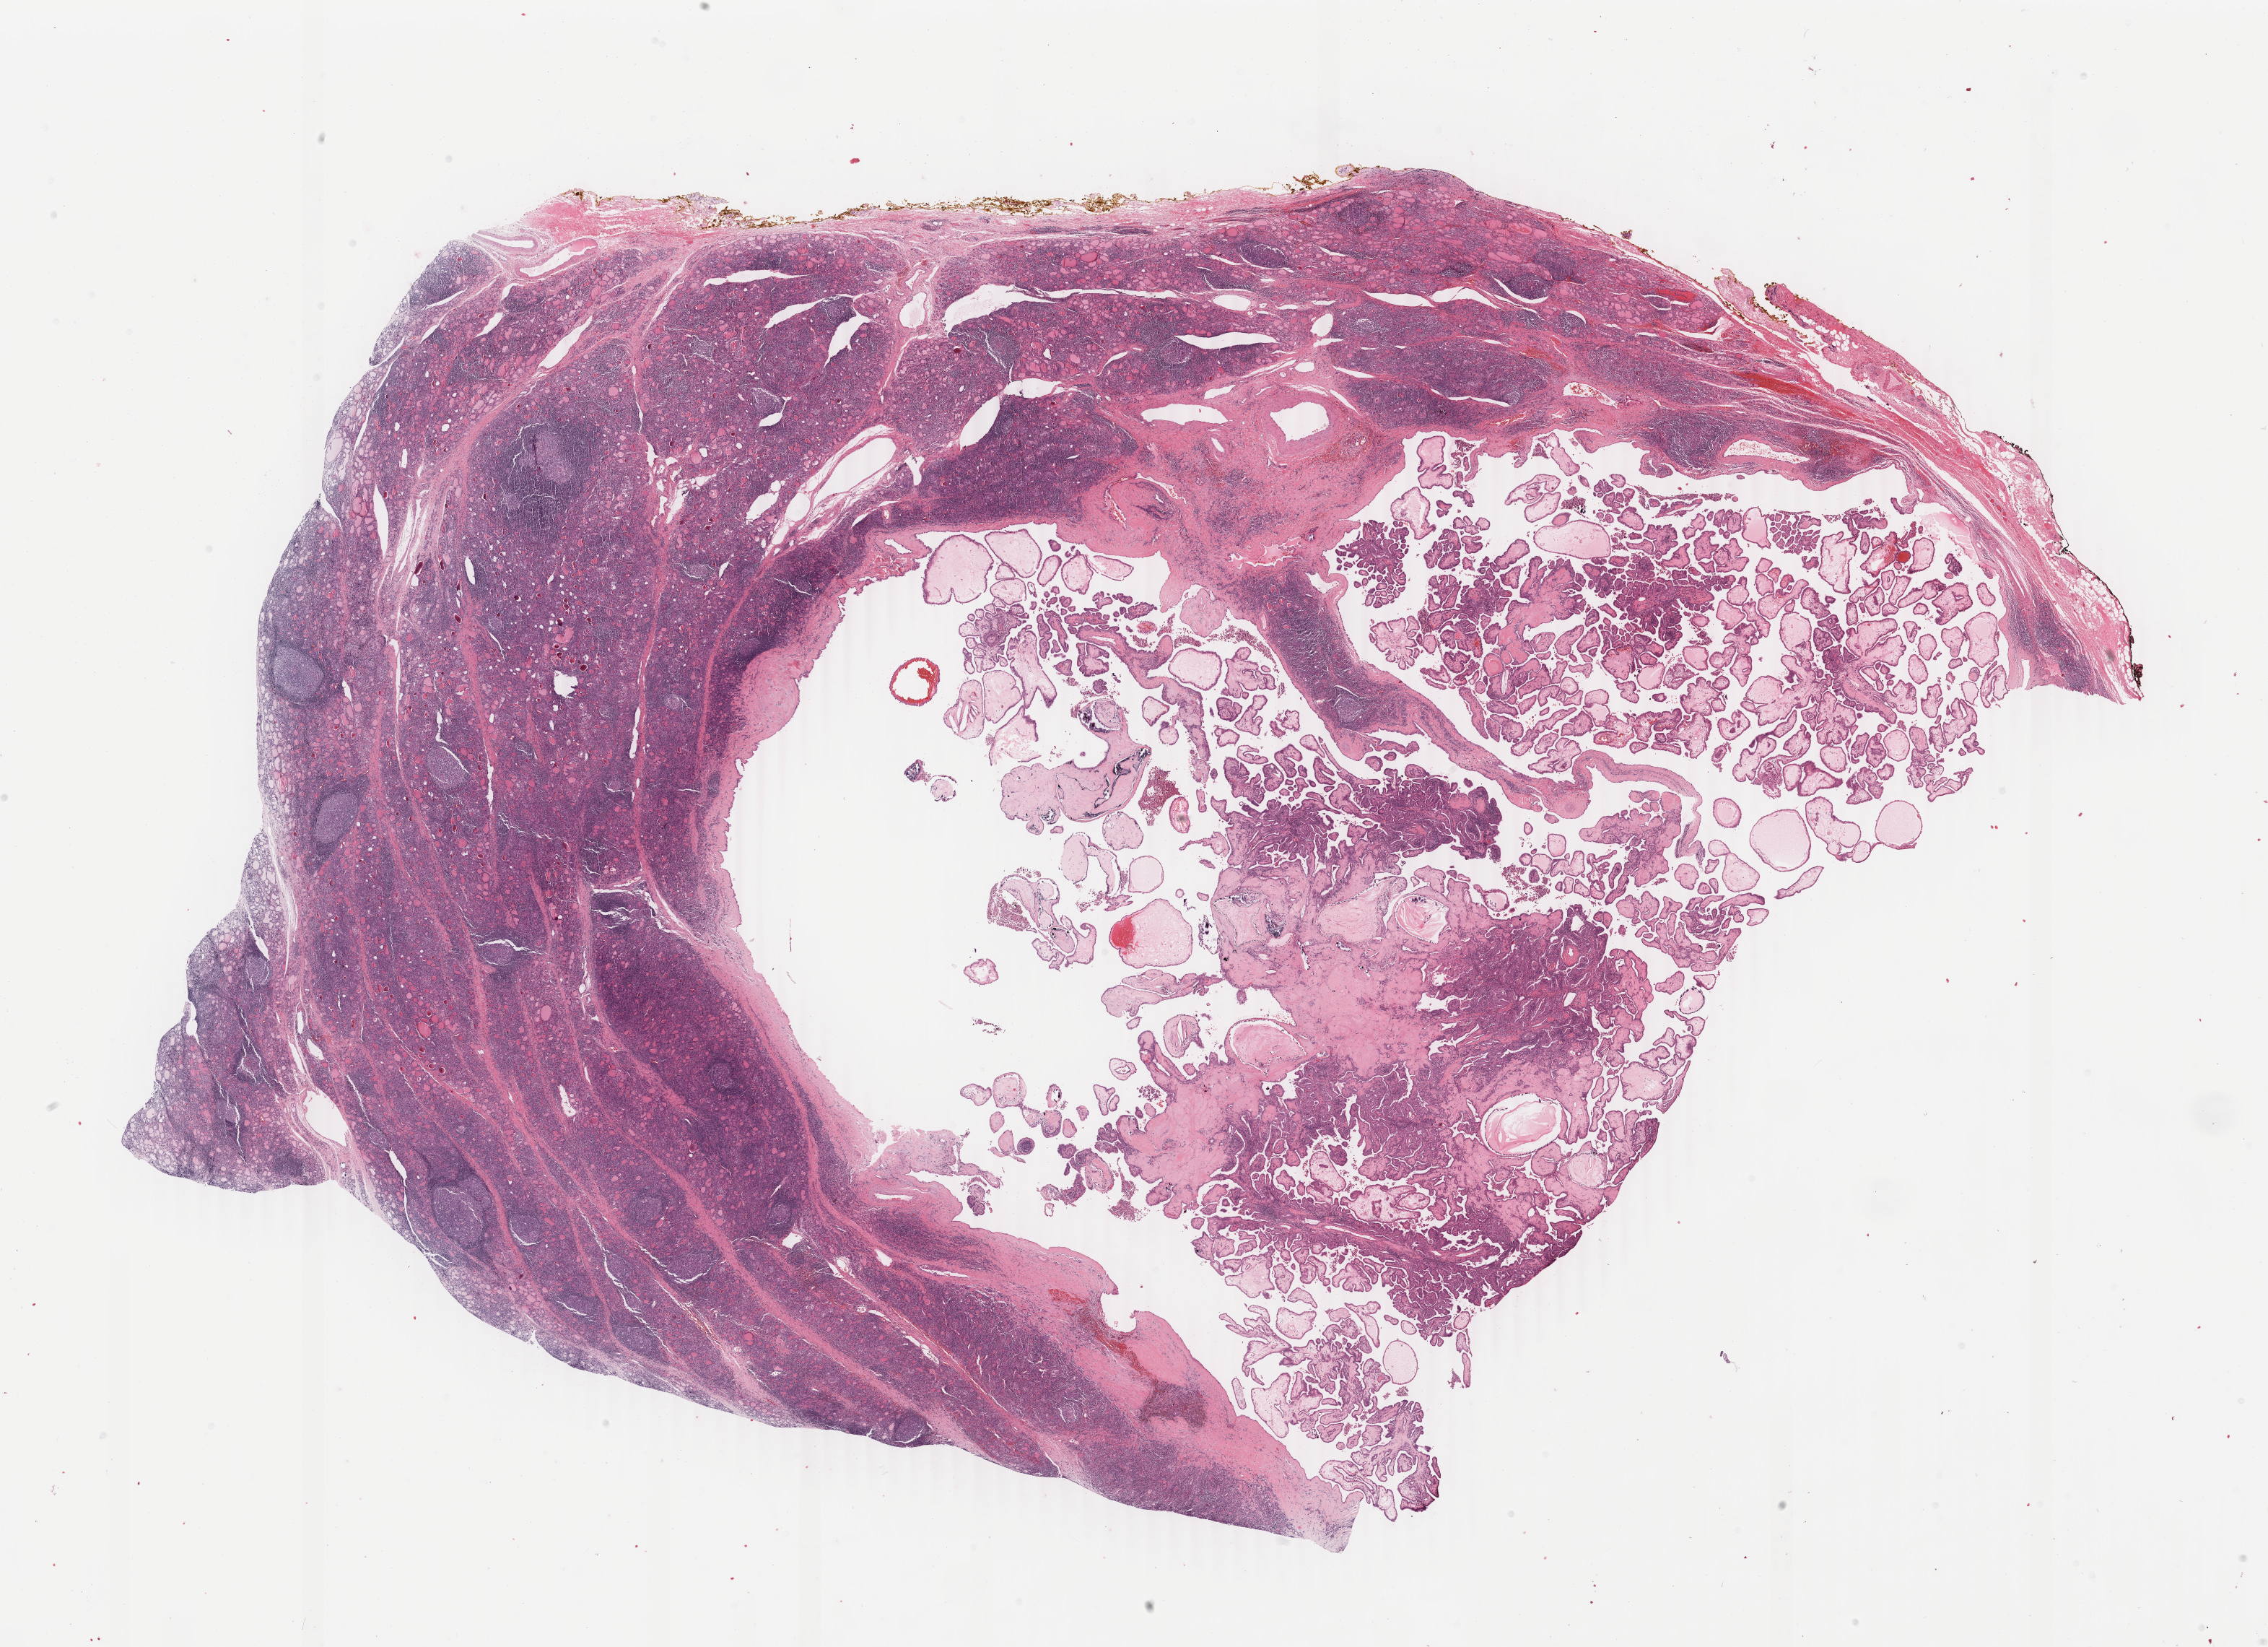
Whole-slide histology image, H&E-stained, a low-resolution overview of the entire scanned area, about 25.0 x 18.1 mm; FFPE section; thyroid, primary tumour sample. Female, age 30 years at initial diagnosis.
• pathologic diagnosis: Papillary adenocarcinoma, NOS (thyroid gland)
• laterality: left
• TNM: T3 N1a MX
• AJCC pathologic stage: I (6th edition)
• lymph nodes positive (case pathology): 3 of 3 examined